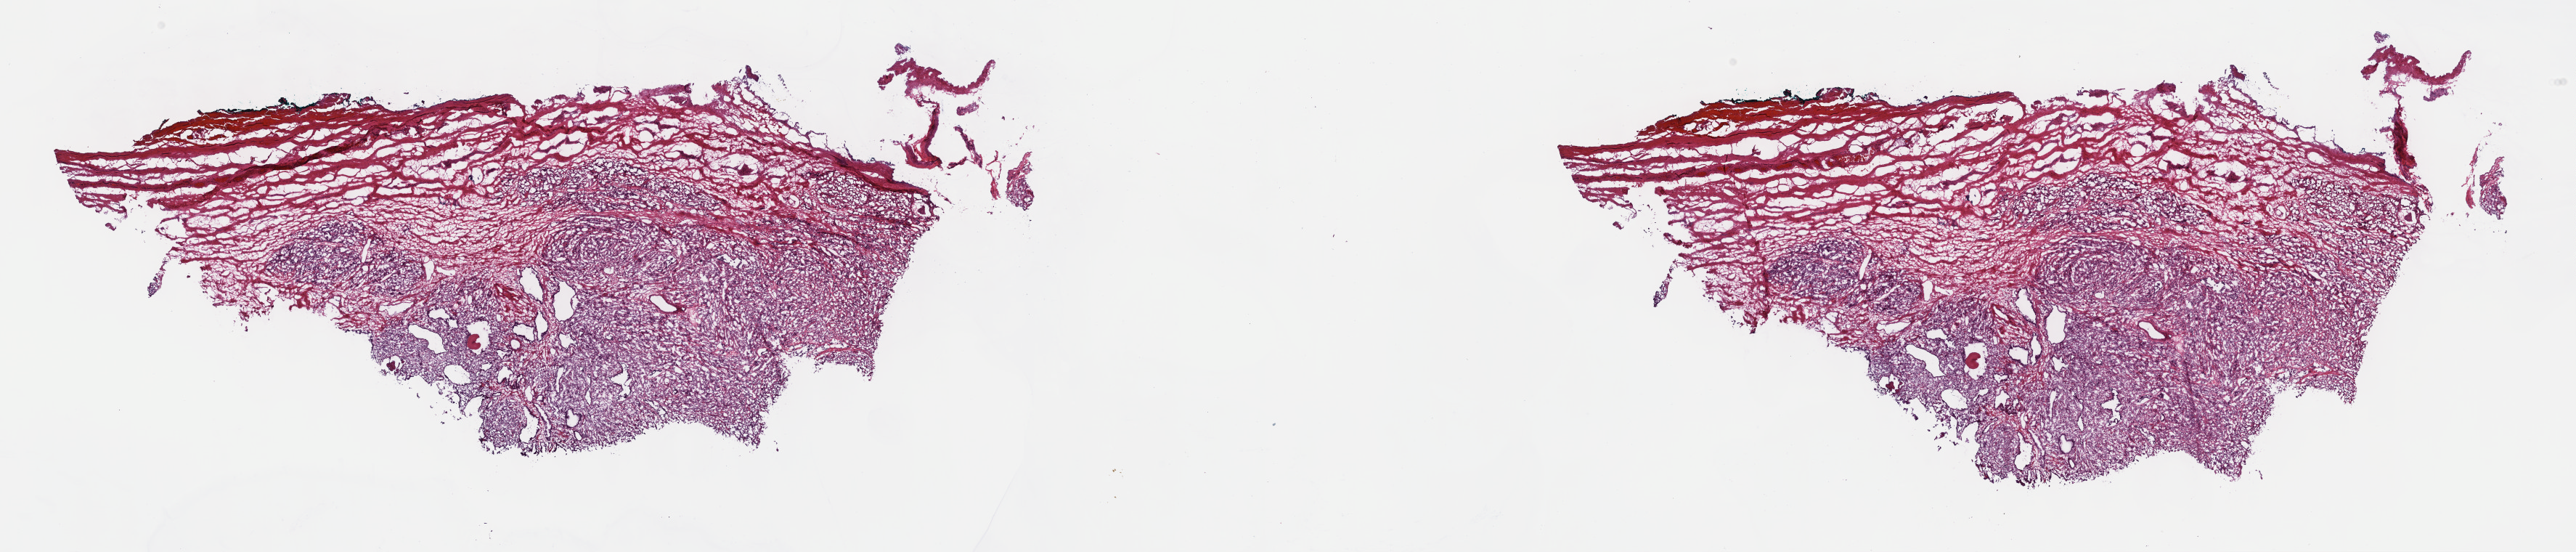
Whole-slide histology image, H&E, a low-resolution overview of the entire scanned area, about 28.7 x 6.1 mm (slide scanned at 40x), frozen section, primary tumour sample from the prostate. Patient: male, age at initial diagnosis 60 years. Gleason score: 9 (4+5). Pathologist review of this section (percent, as recorded): tumour cells 70%, tumour nuclei 80%, normal cells 5%, stromal cells 25%, necrosis 0%. Infiltration values recorded for this section: lymphocyte infiltration 0%, monocyte infiltration 0%, neutrophil infiltration 0%.
Laterality: bilateral. Diagnosis: Adenocarcinoma, NOS (prostate gland). Lymph nodes positive (case pathology): 1 of 11 examined.